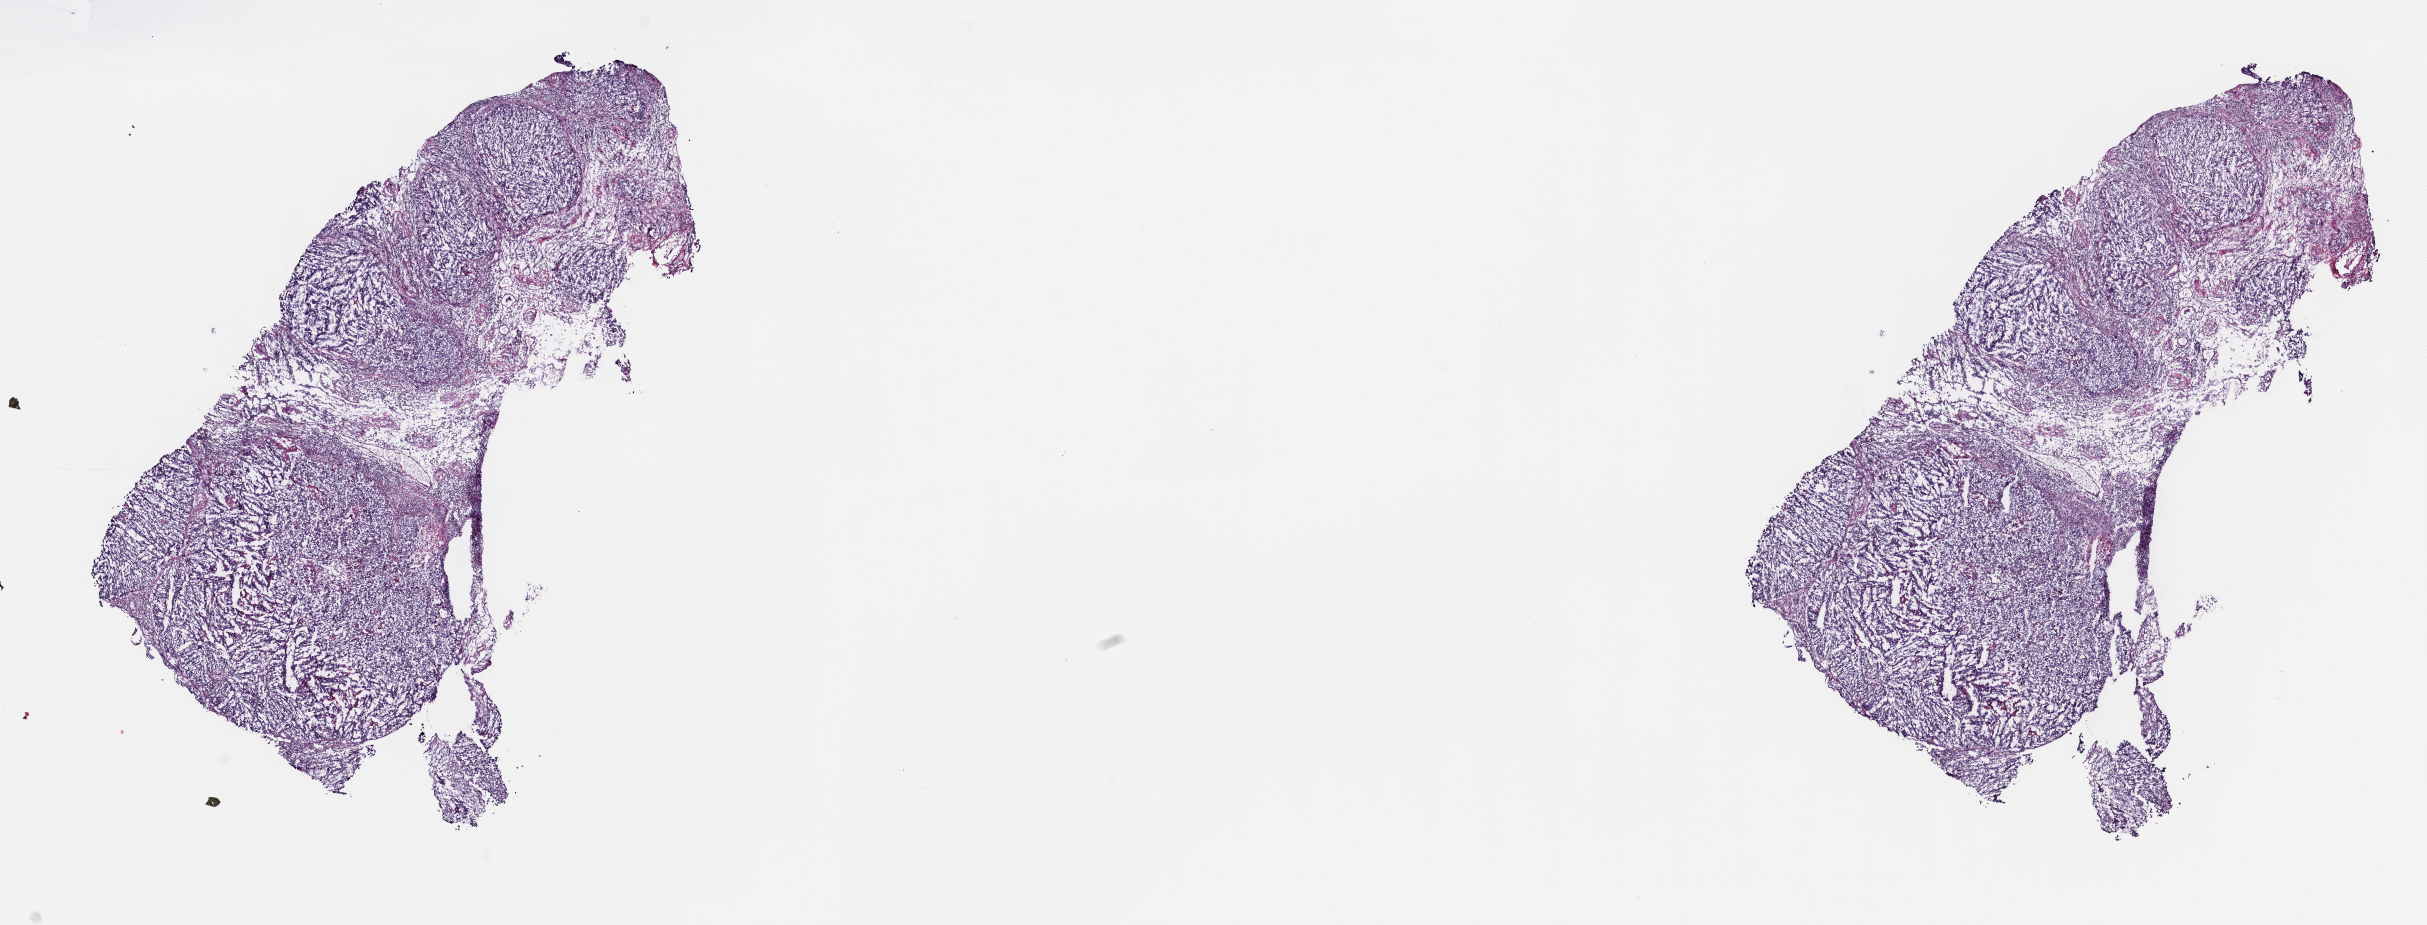
Whole-slide histology image, Hematoxylin and eosin (H&E) stained, low-resolution overview of the scanned area, about 19.6 x 7.5 mm, frozen section from the top of the tissue portion, testis, primary tumour sample. Patient: male, age at initial diagnosis 31 years. Pathologist review of this section (percent, as recorded): tumour cells 95%, tumour nuclei 75%, normal cells 0%, stromal cells 0%, necrosis 5%. Infiltration values recorded for this section: lymphocyte infiltration 0%, monocyte infiltration 0%, neutrophil infiltration 0%.
• pathologic diagnosis: Embryonal carcinoma, NOS
• AJCC pathologic stage: IIA (7th edition)
• laterality: right